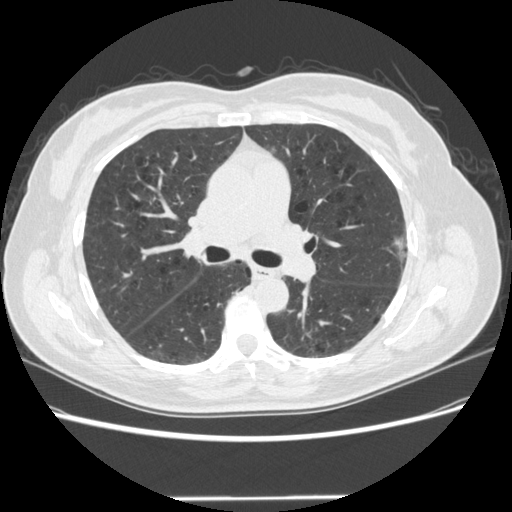
Chest CT (low-dose screening protocol), one axial image; first (baseline) screen; lung window (W 1500 / L -600 HU). Female, age 61 years at enrolment.
Expert reader's lesion annotation, bounding box [x1, y1, x2, y2] px = [382, 227, 426, 278]. Screening reader's record for this exam: no non-calcified nodule ≥4 mm recorded. Official screen result: negative screen, minor abnormalities not suspicious for lung cancer. Later outcome: lung cancer diagnosed 791 days after this screen — bronchiolo-alveolar adenocarcinoma, NOS, left upper lobe, well differentiated (G1), stage IA (AJCC 6th edition), 11 mm at pathology.